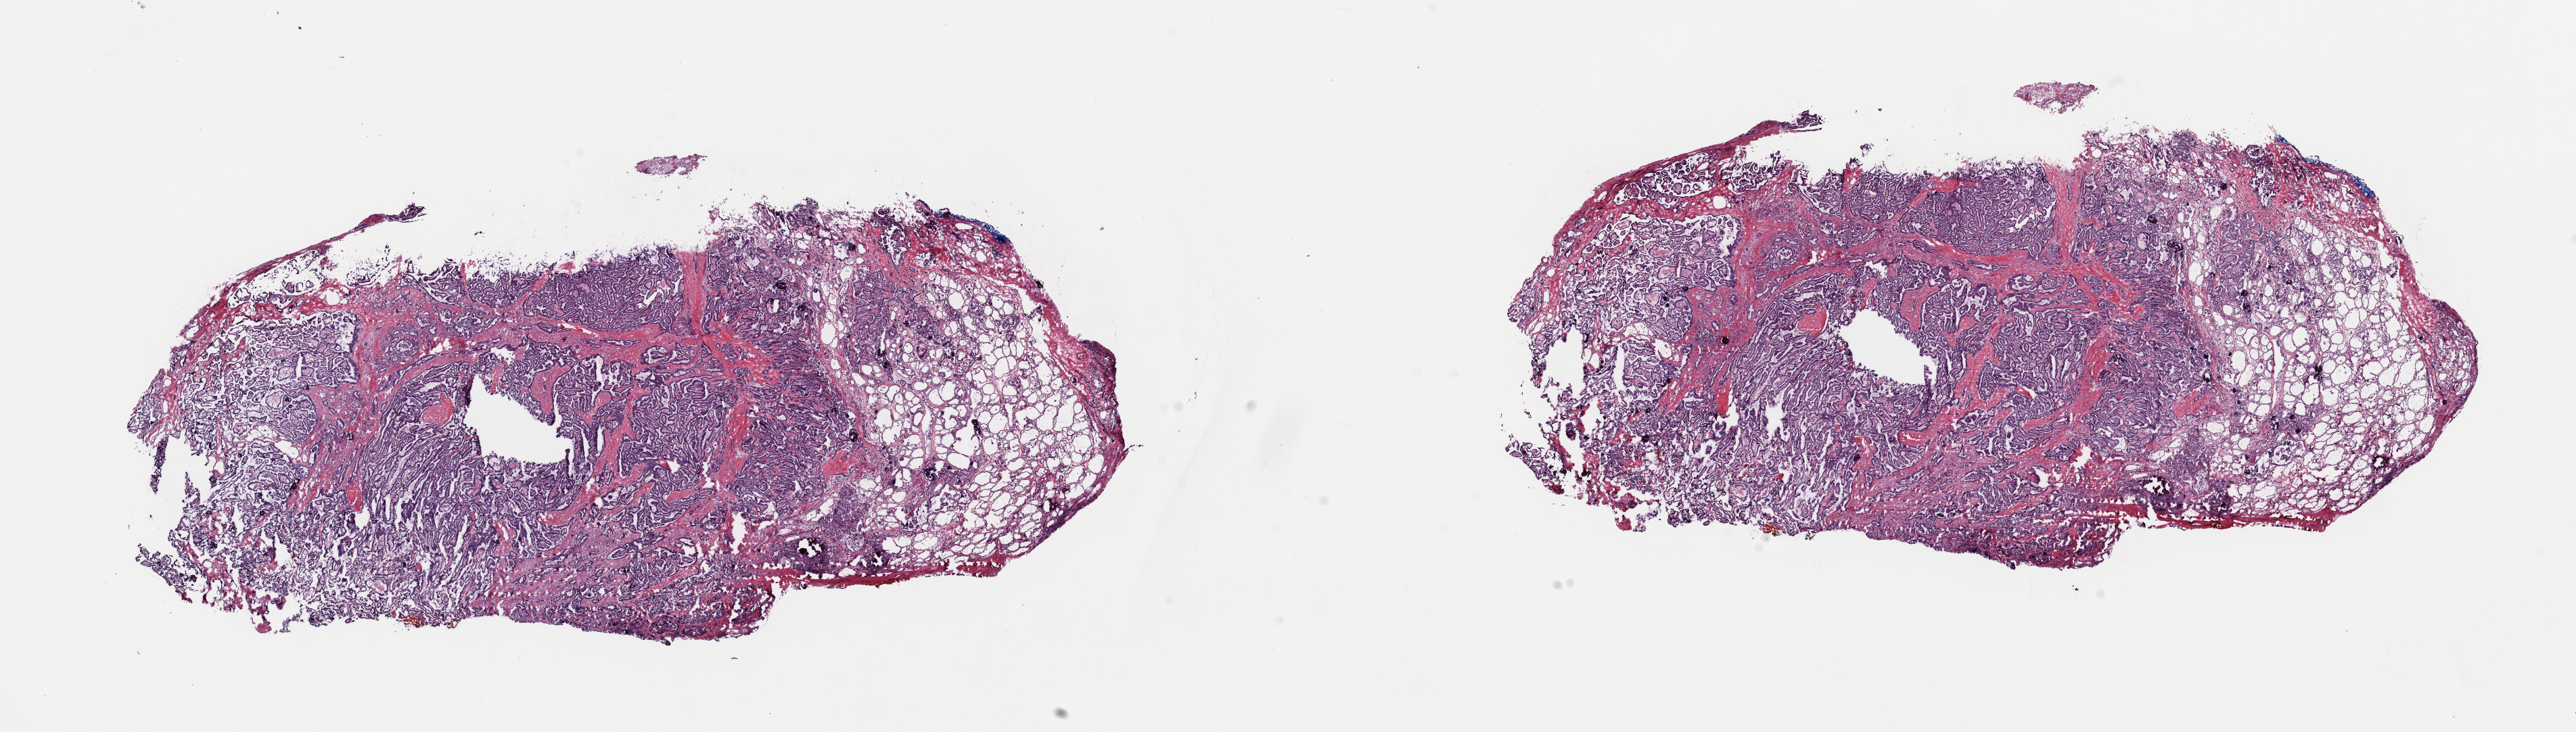
H&E whole-slide image — whole scanned area (about 30.1 x 8.5 mm, acquisition: 40x scan) shown as a low-resolution overview, frozen section, sample: primary tumour, thyroid. Male patient; age at initial diagnosis 60 years. Composition of this section per pathologist review: tumour cells 60%, tumour nuclei 90%, normal cells 10%, stromal cells 30%, necrosis 0%. Infiltration values recorded for this section: lymphocyte infiltration 1%, monocyte infiltration 2%, neutrophil infiltration 0%.
Lymph nodes positive (case pathology): 31 of 99 examined. AJCC pathologic stage: IVA. Diagnosis: Nonencapsulated sclerosing carcinoma (thyroid gland).